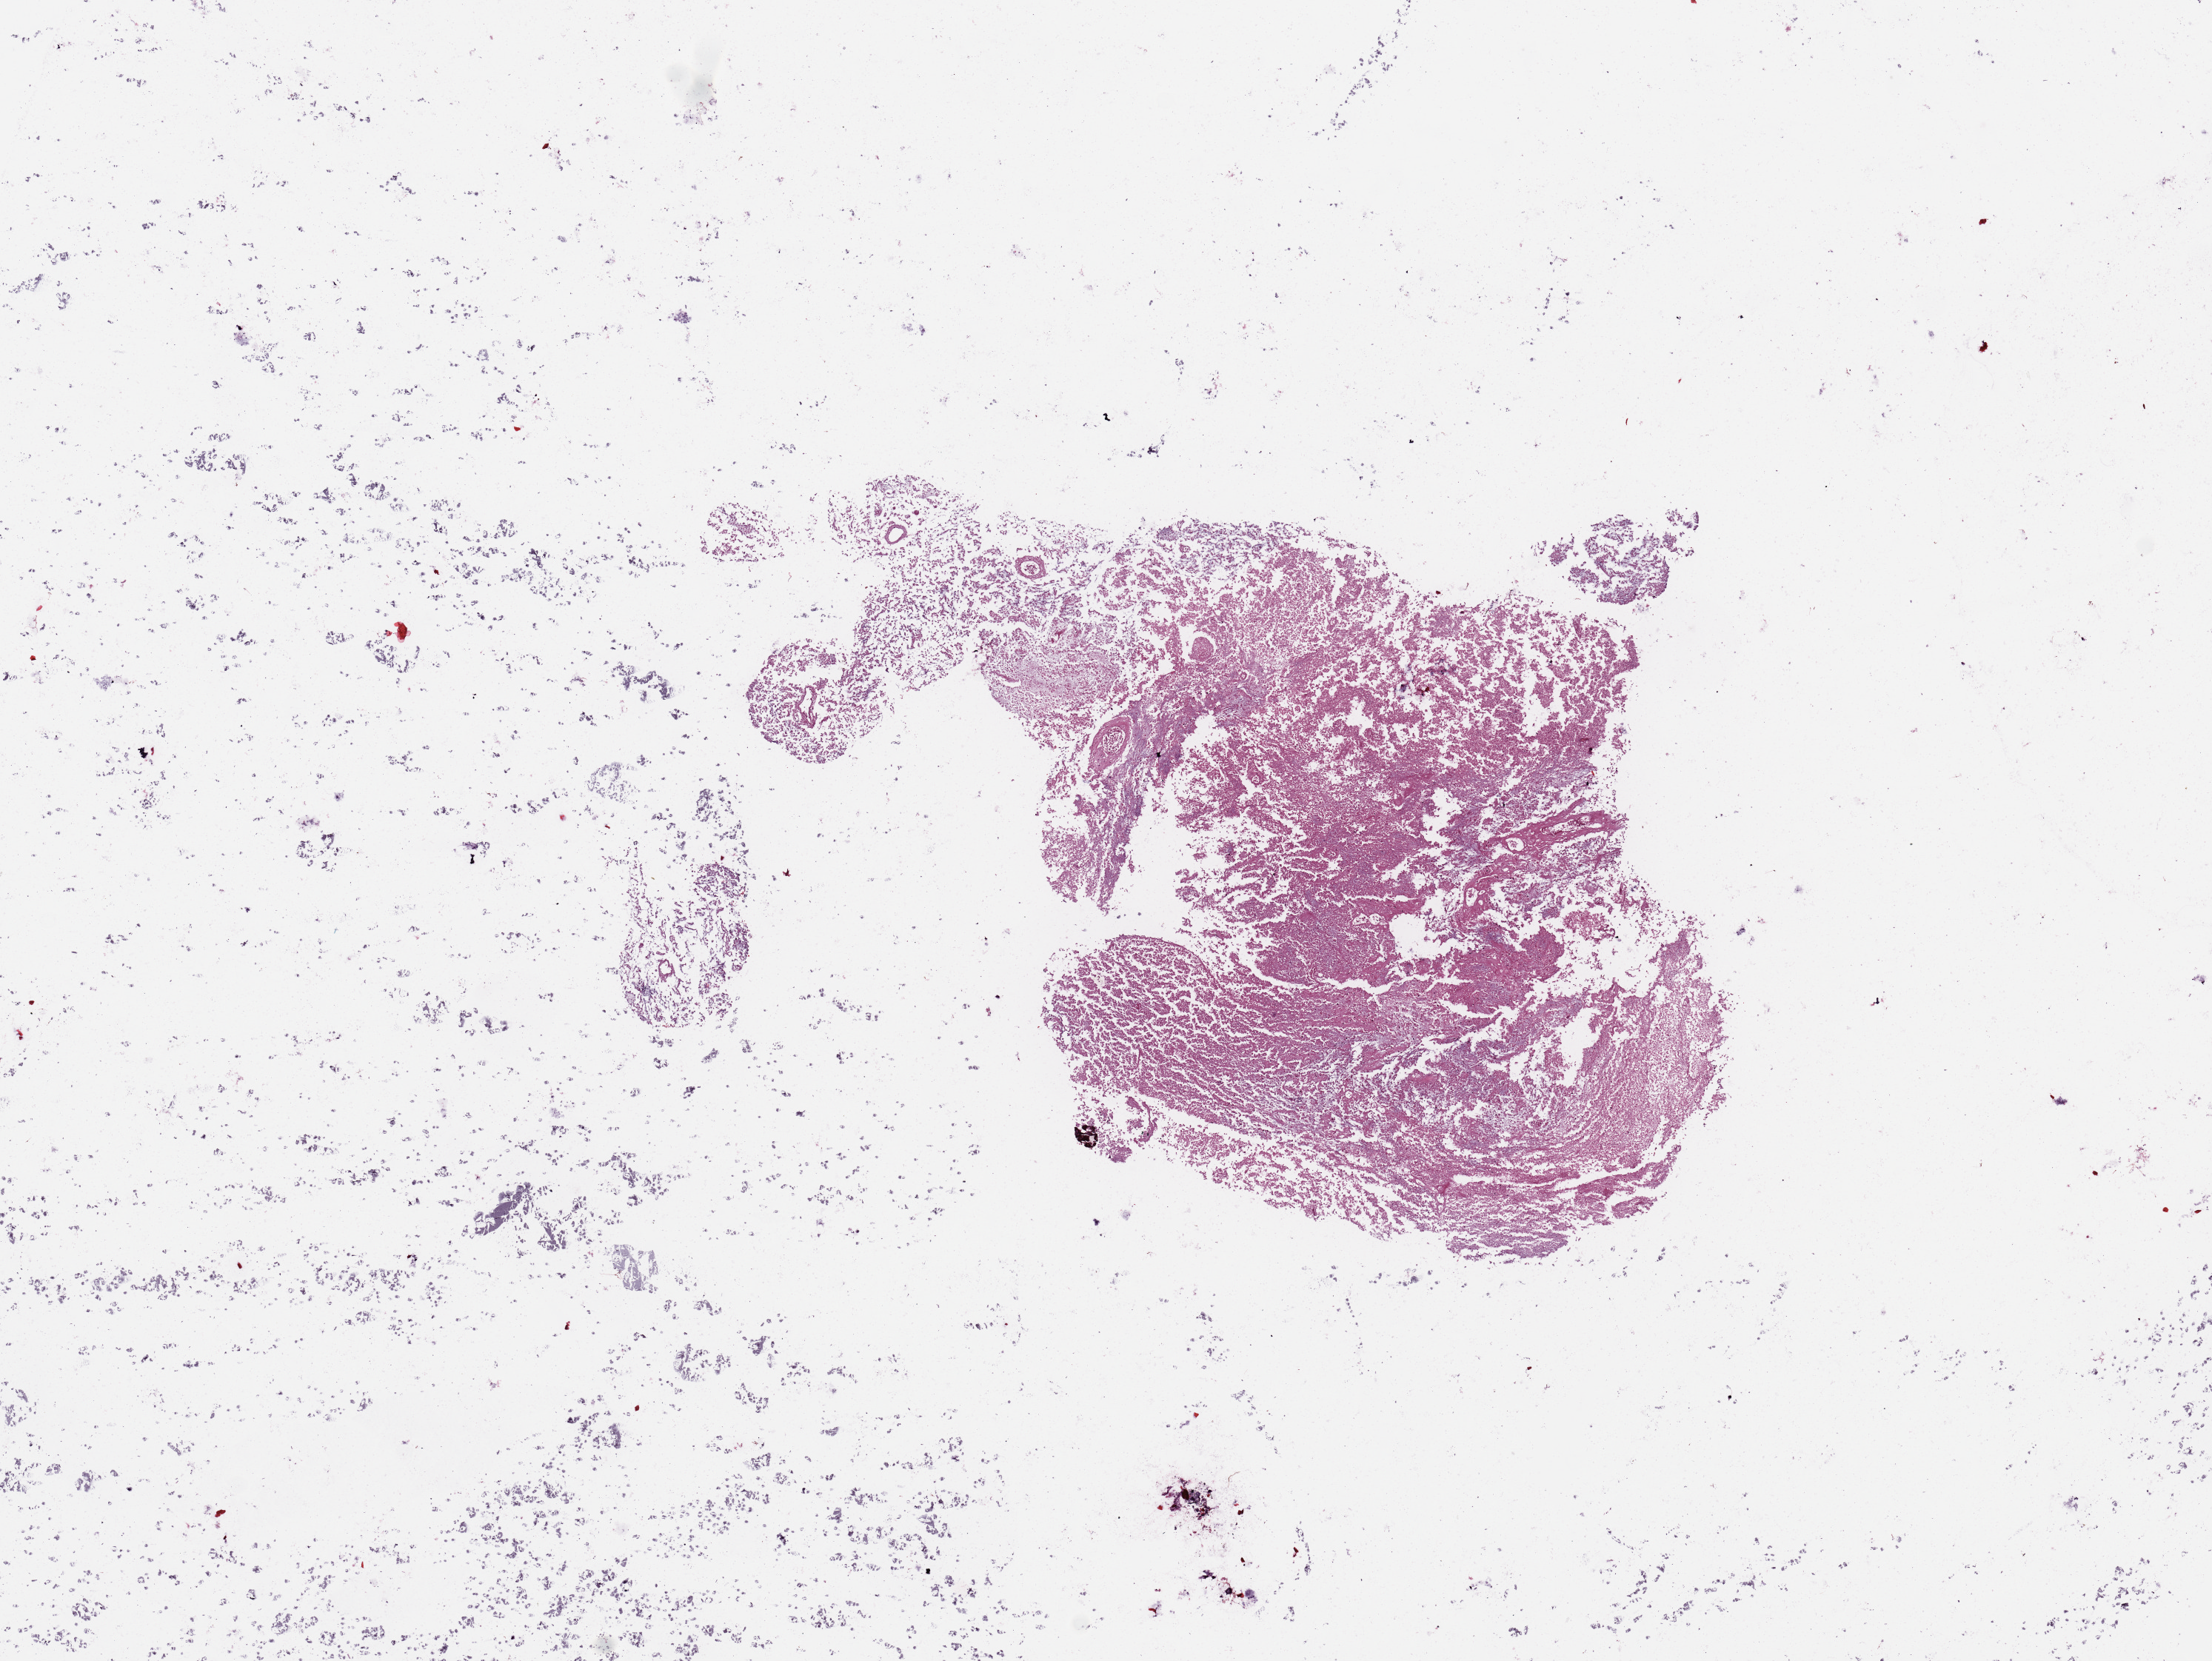
Whole-slide histology image, Hematoxylin and eosin (H&E) stained — whole scanned area (about 11.8 x 8.9 mm, slide scanned at 20x) shown as a low-resolution overview; brain, tumour tissue. Female, 24 y/o.
Histologic diagnosis: Glioblastoma.